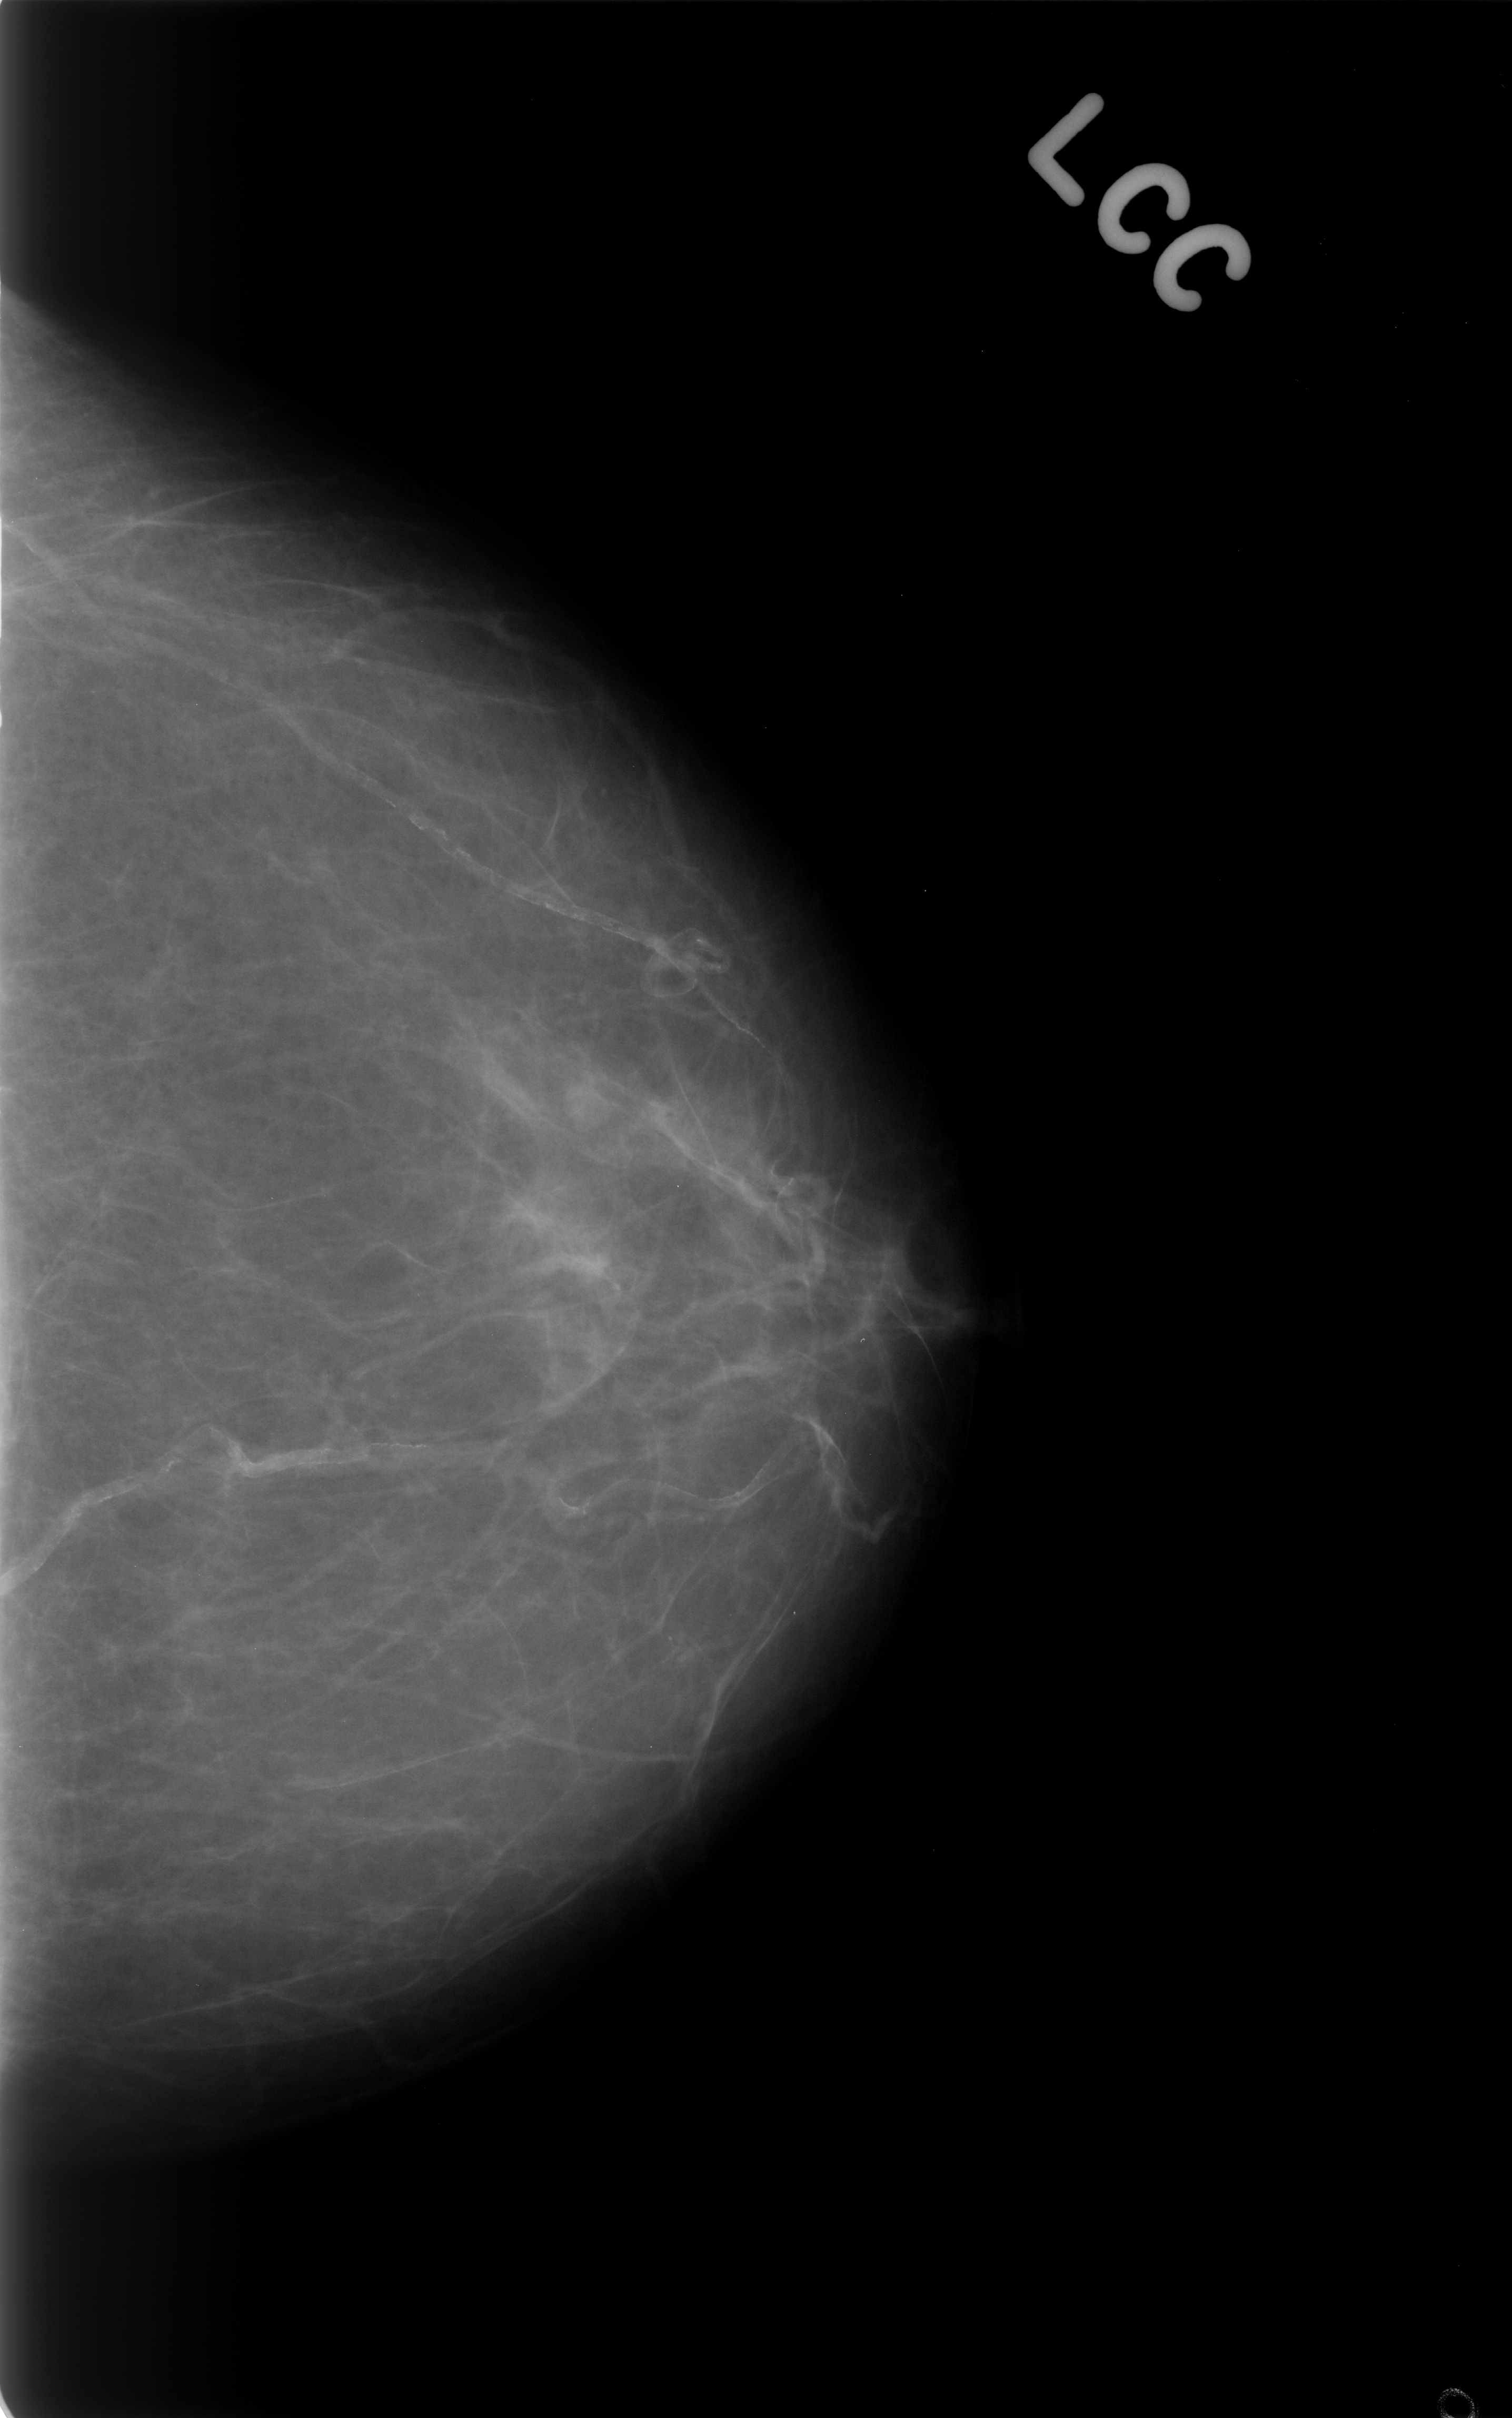
Scanned film-screen mammogram; left breast; craniocaudal (CC) view; BI-RADS breast density category 1 (scale 1–4); 1512 × 2418 image matrix.
Expert-marked regions of interest on this image (one box per marked abnormality):
- mass, shape lobulated, margins circumscribed; BI-RADS assessment category 3; pathology result (as recorded, not read from the image): benign: bounding box (x1, y1, x2, y2) in pixels: (530, 1038, 633, 1149)